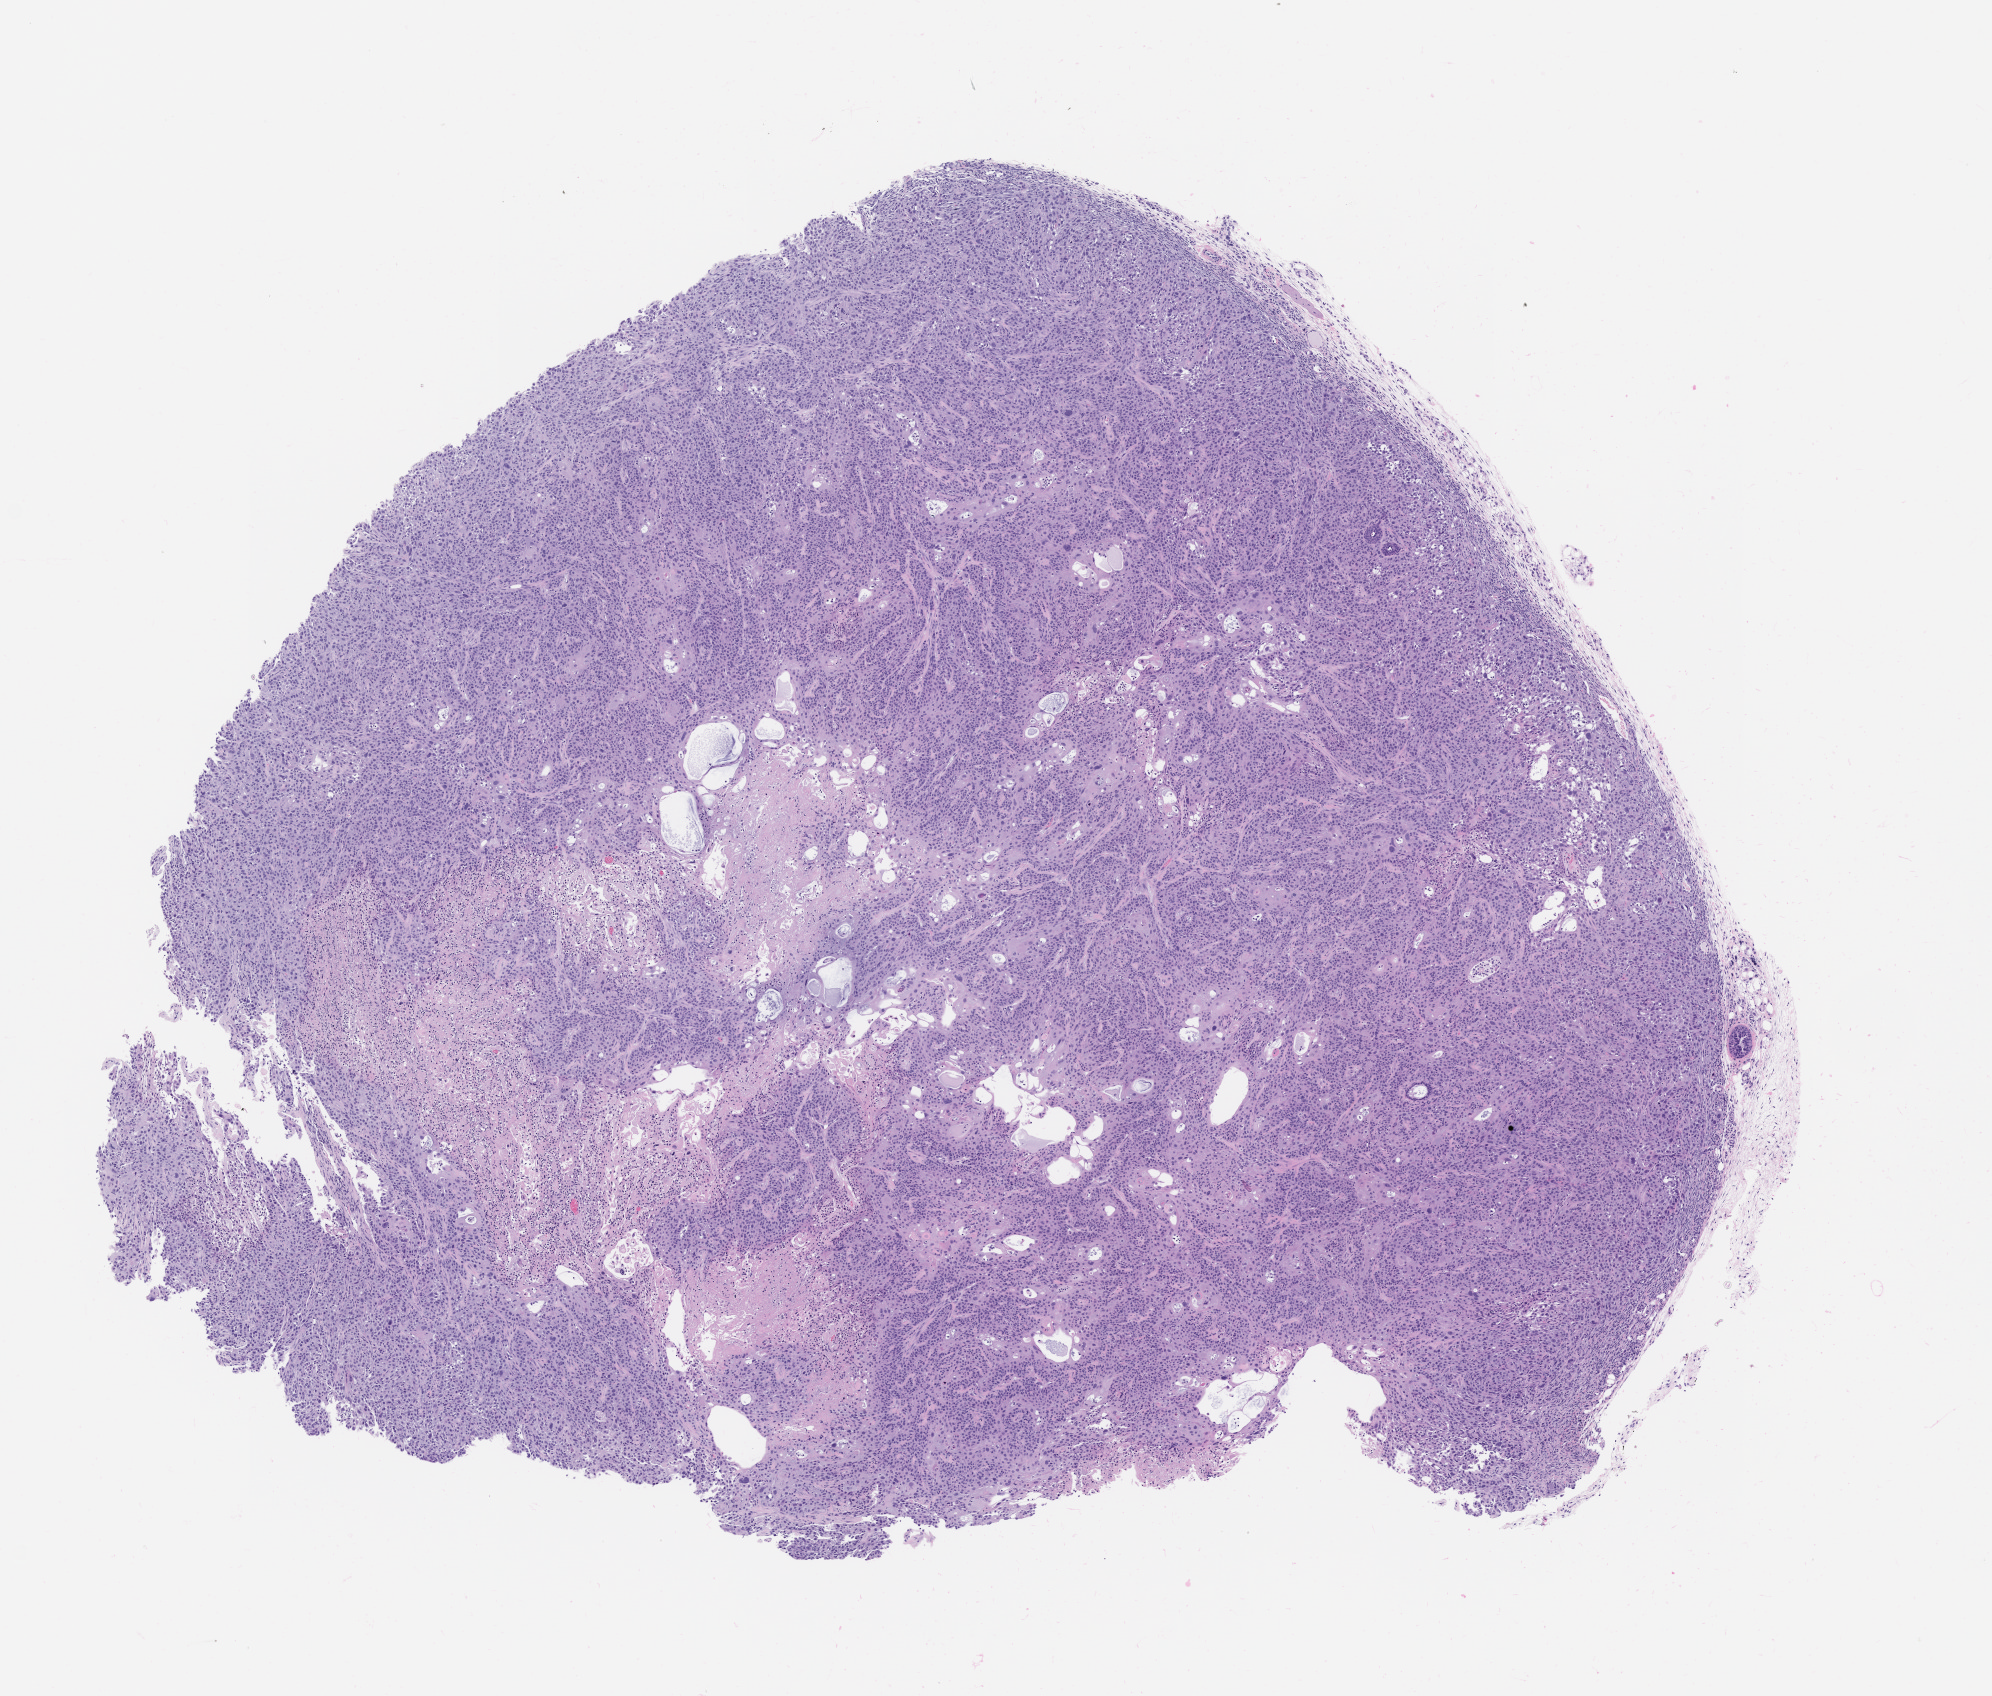
H&E whole-slide image of a patient-derived xenograft (PDX) tumor grown in a mouse, passage 1 — shown as a low-resolution overview of the whole scanned area (about 8.0 x 6.8 mm). FFPE section. Originating tumor site category: head and neck.
* originating patient diagnosis: Mucoepidermoid Carcinoma